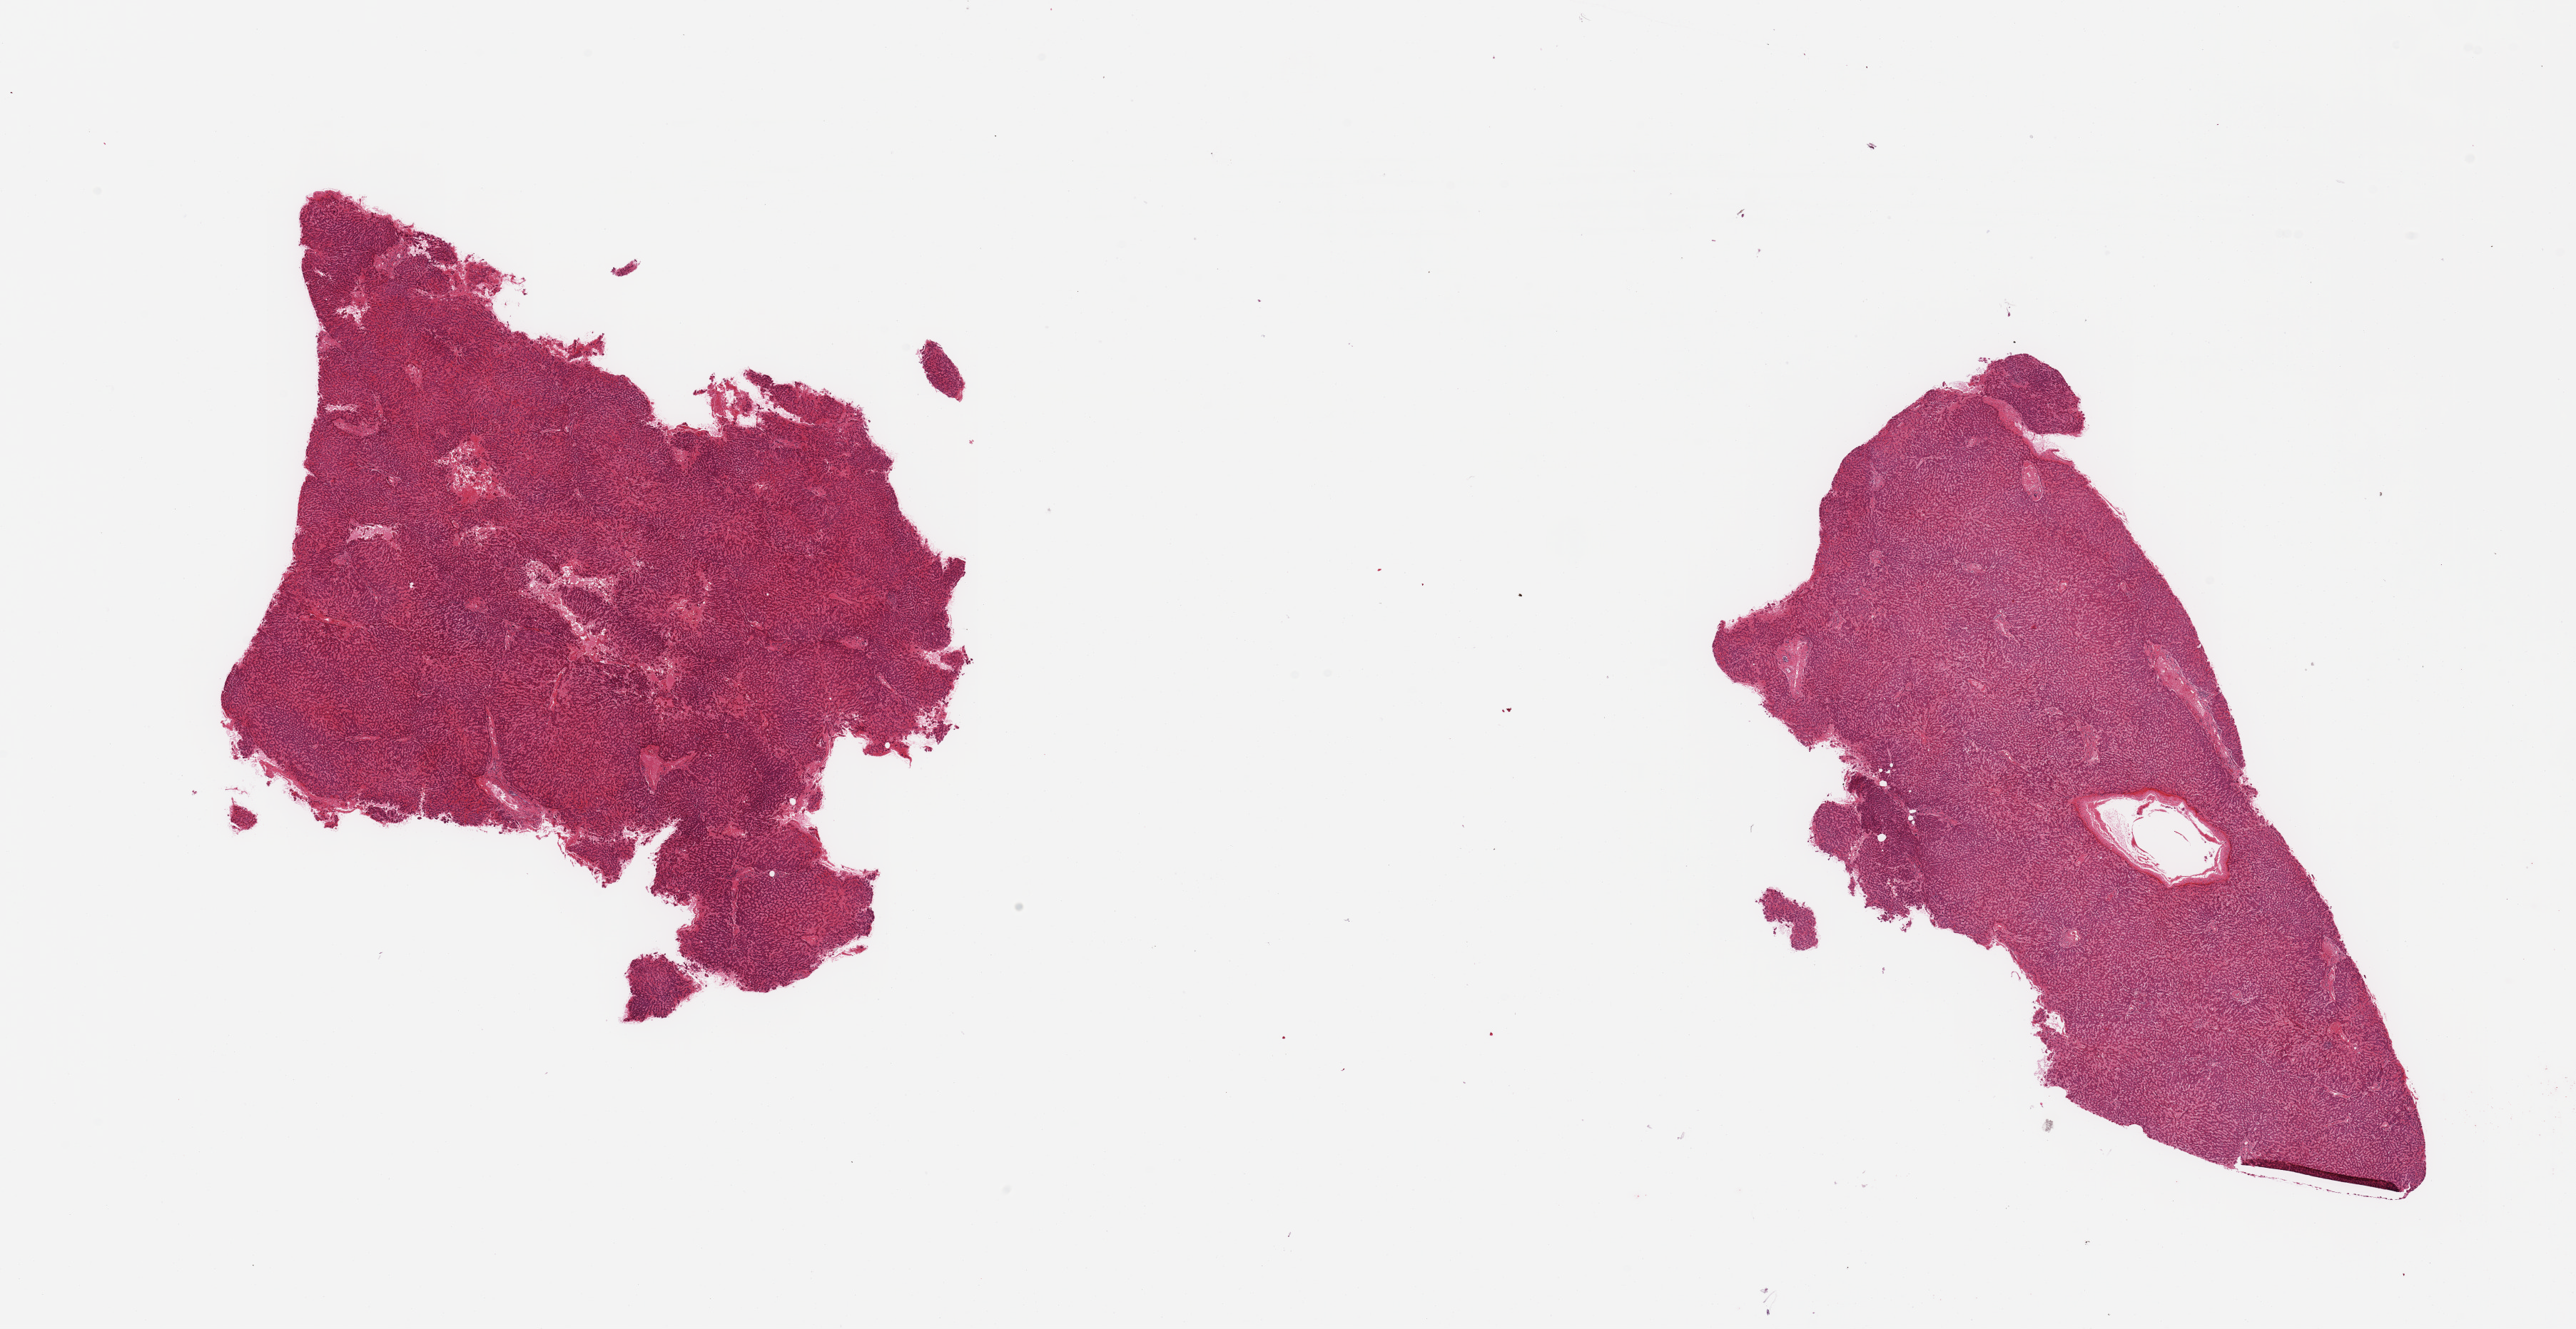
Whole-slide image, hematoxylin and eosin (H&E) stain, brightfield — low-resolution overview of the scanned area, about 28.5 x 14.7 mm; PAXgene-fixed, paraffin-embedded tissue; target tissue: liver; donor tissue sample.
• reviewer comment on this tissue sample: 2 pieces; congested